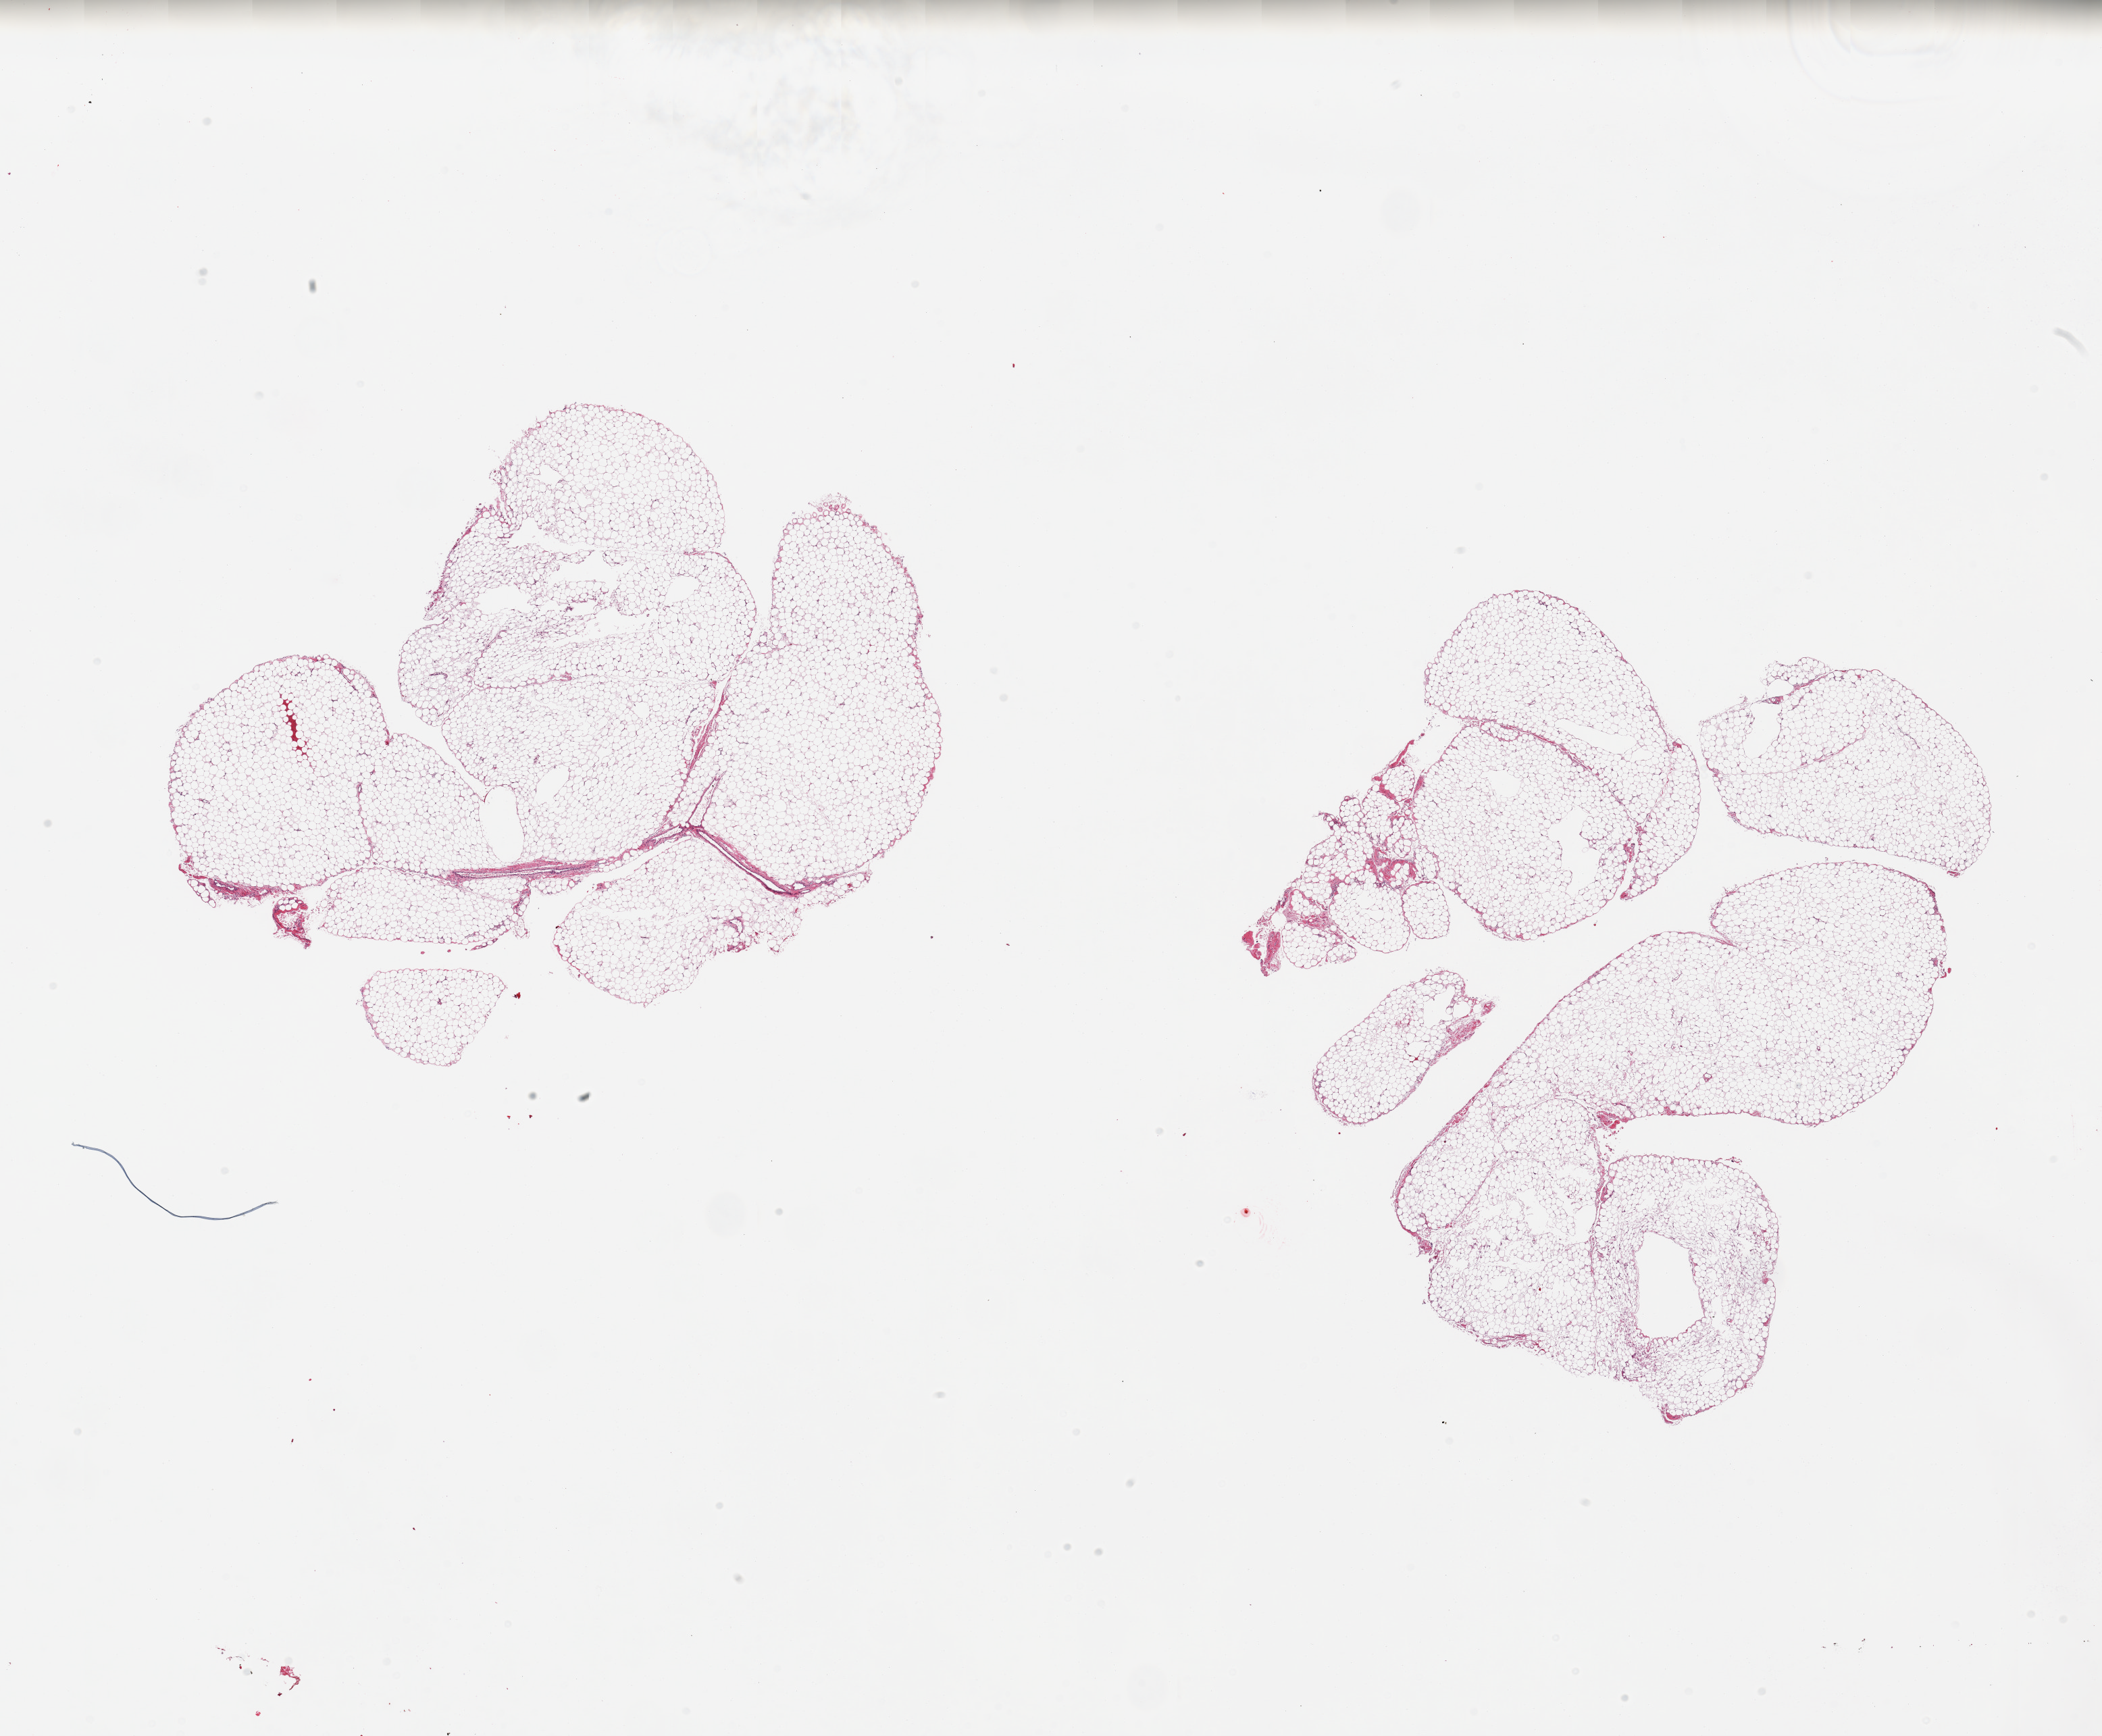
Haematoxylin and eosin whole-slide image — a low-resolution overview of the entire scanned area, about 24.6 x 20.3 mm, PAXgene-fixed paraffin-embedded (PFPE) section, section of omentum (target tissue), tissue donor sample. Donor sex: female.
Review note (as recorded): 2 pieces.